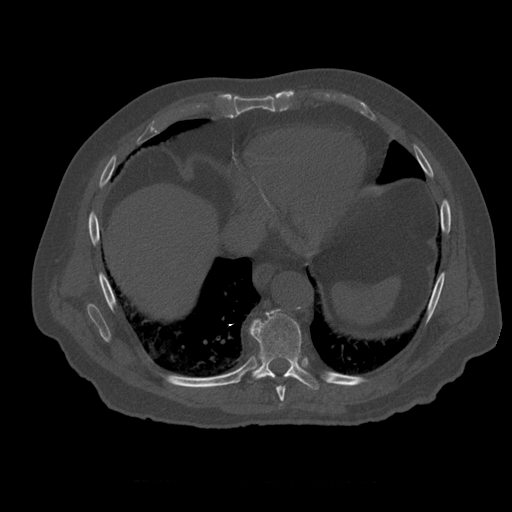
CT including the spine, one axial slice. Position 326 of 399 along the scan axis. Bone window (W 1800 / L 400 HU). 512 × 512 image matrix, field of view 407 × 407 mm. Patient age 73 years. From the clinical record (not read from this slice): primary cancer: prostate.
Outlined on this slice (semi-automatic segmentation, software-assisted and operator-edited):
- T8 vertebra: box from (x=265, y=377) to (x=289, y=408) px
- T9 vertebra: (x=249, y=309)–(x=320, y=391)